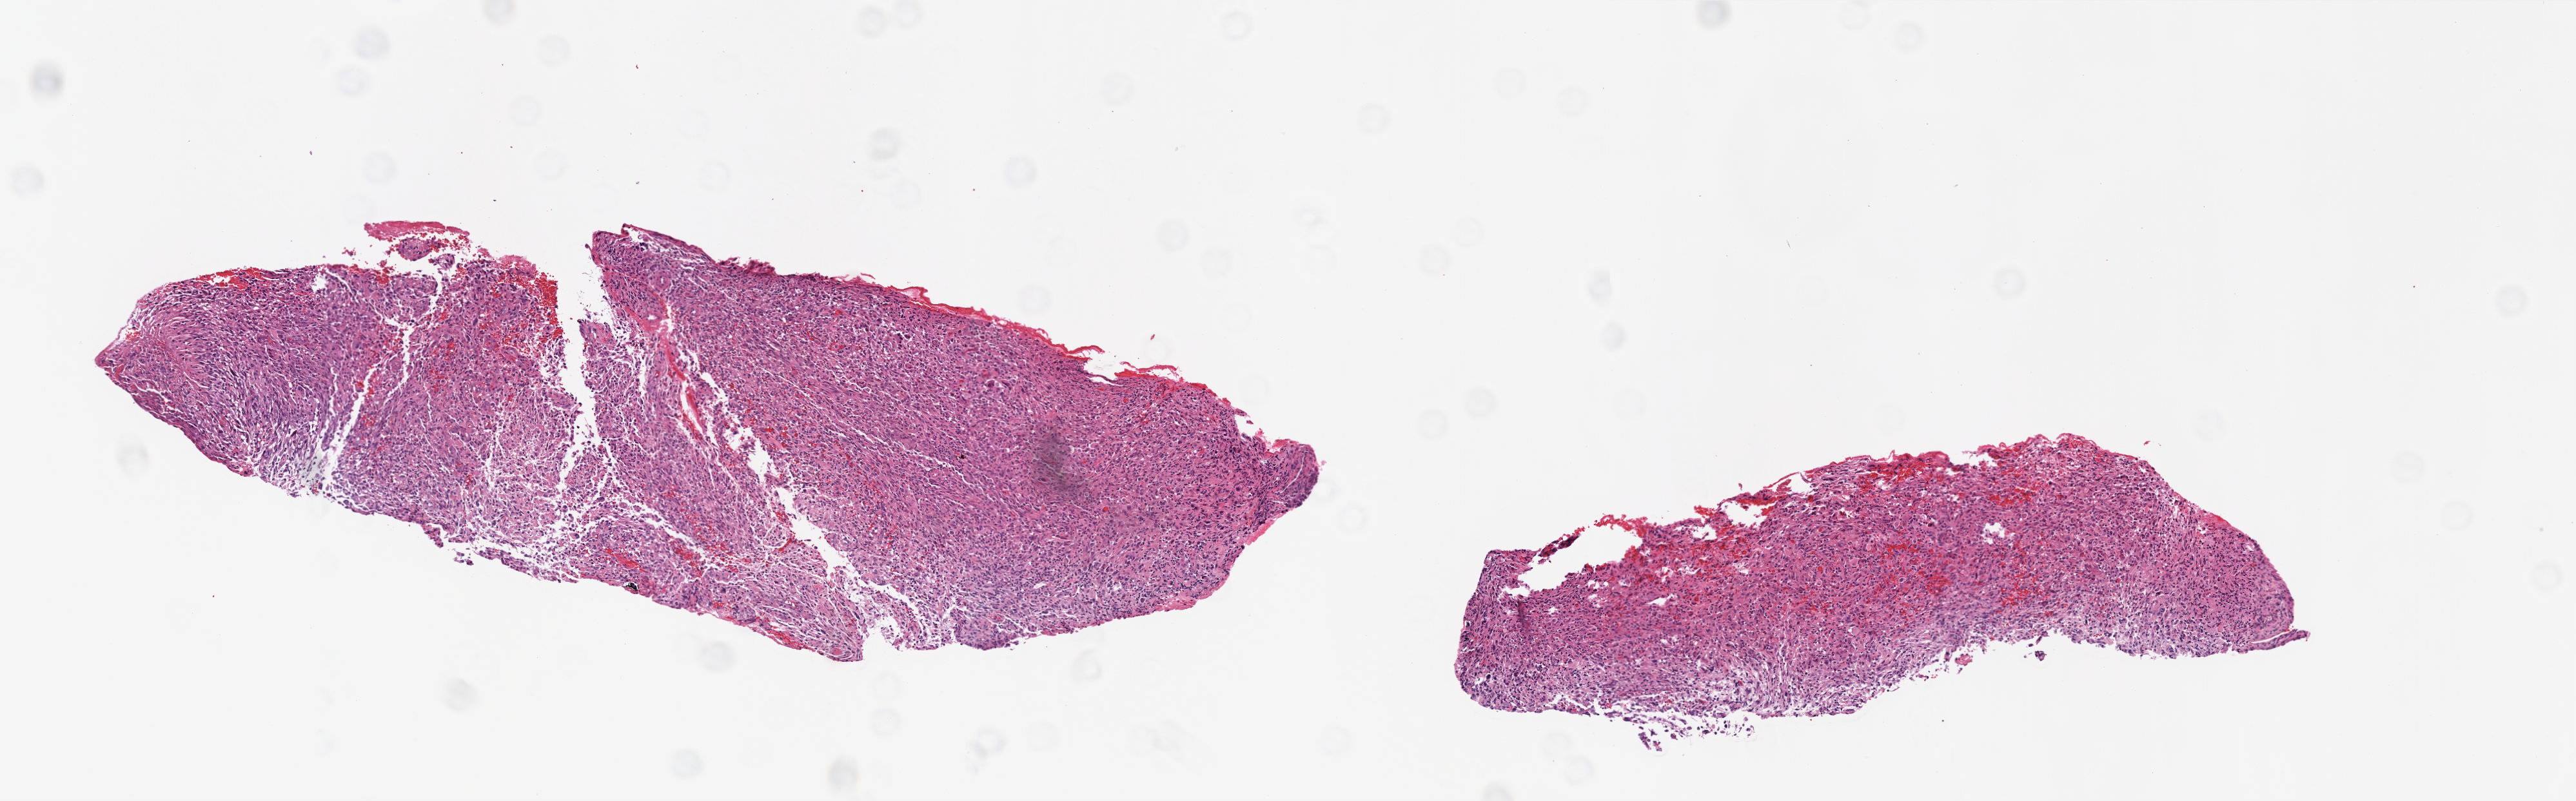
Digitized H&E tissue section (whole slide) — shown as a low-resolution overview of the whole scanned area (about 8.0 x 2.5 mm, from a 20x scan); formalin-fixed paraffin-embedded (FFPE) diagnostic section; primary tumour sample from the brain. Male patient; age at initial diagnosis 40 years.
* pathologic diagnosis: Glioblastoma